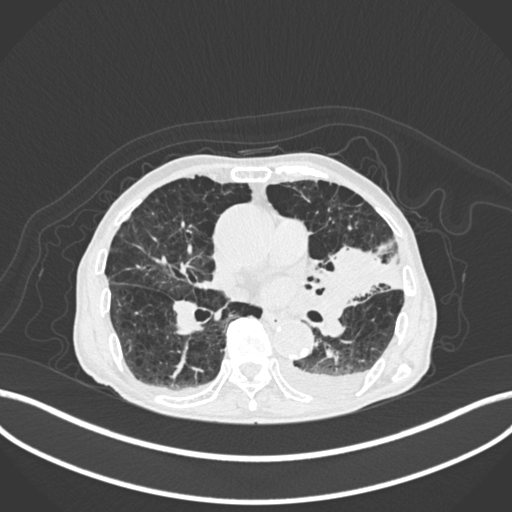
Chest CT, one axial slice. Position 108 of 400 along the scan axis. 120 kVp. Lung window (W 1500 / L -600 HU). 1 mm slice thickness. 512 × 512 image matrix, field of view 400 × 400 mm. Patient: male, 90 years or older. Case-level facts recorded for this patient, not image findings: clinical TNM (as recorded): T2b N1 M0.
Annotated regions visible in this slice (bounding box drawn by a radiologist):
- lung tumour (recorded histology: squamous cell carcinoma): box from (x=329, y=234) to (x=389, y=303) px